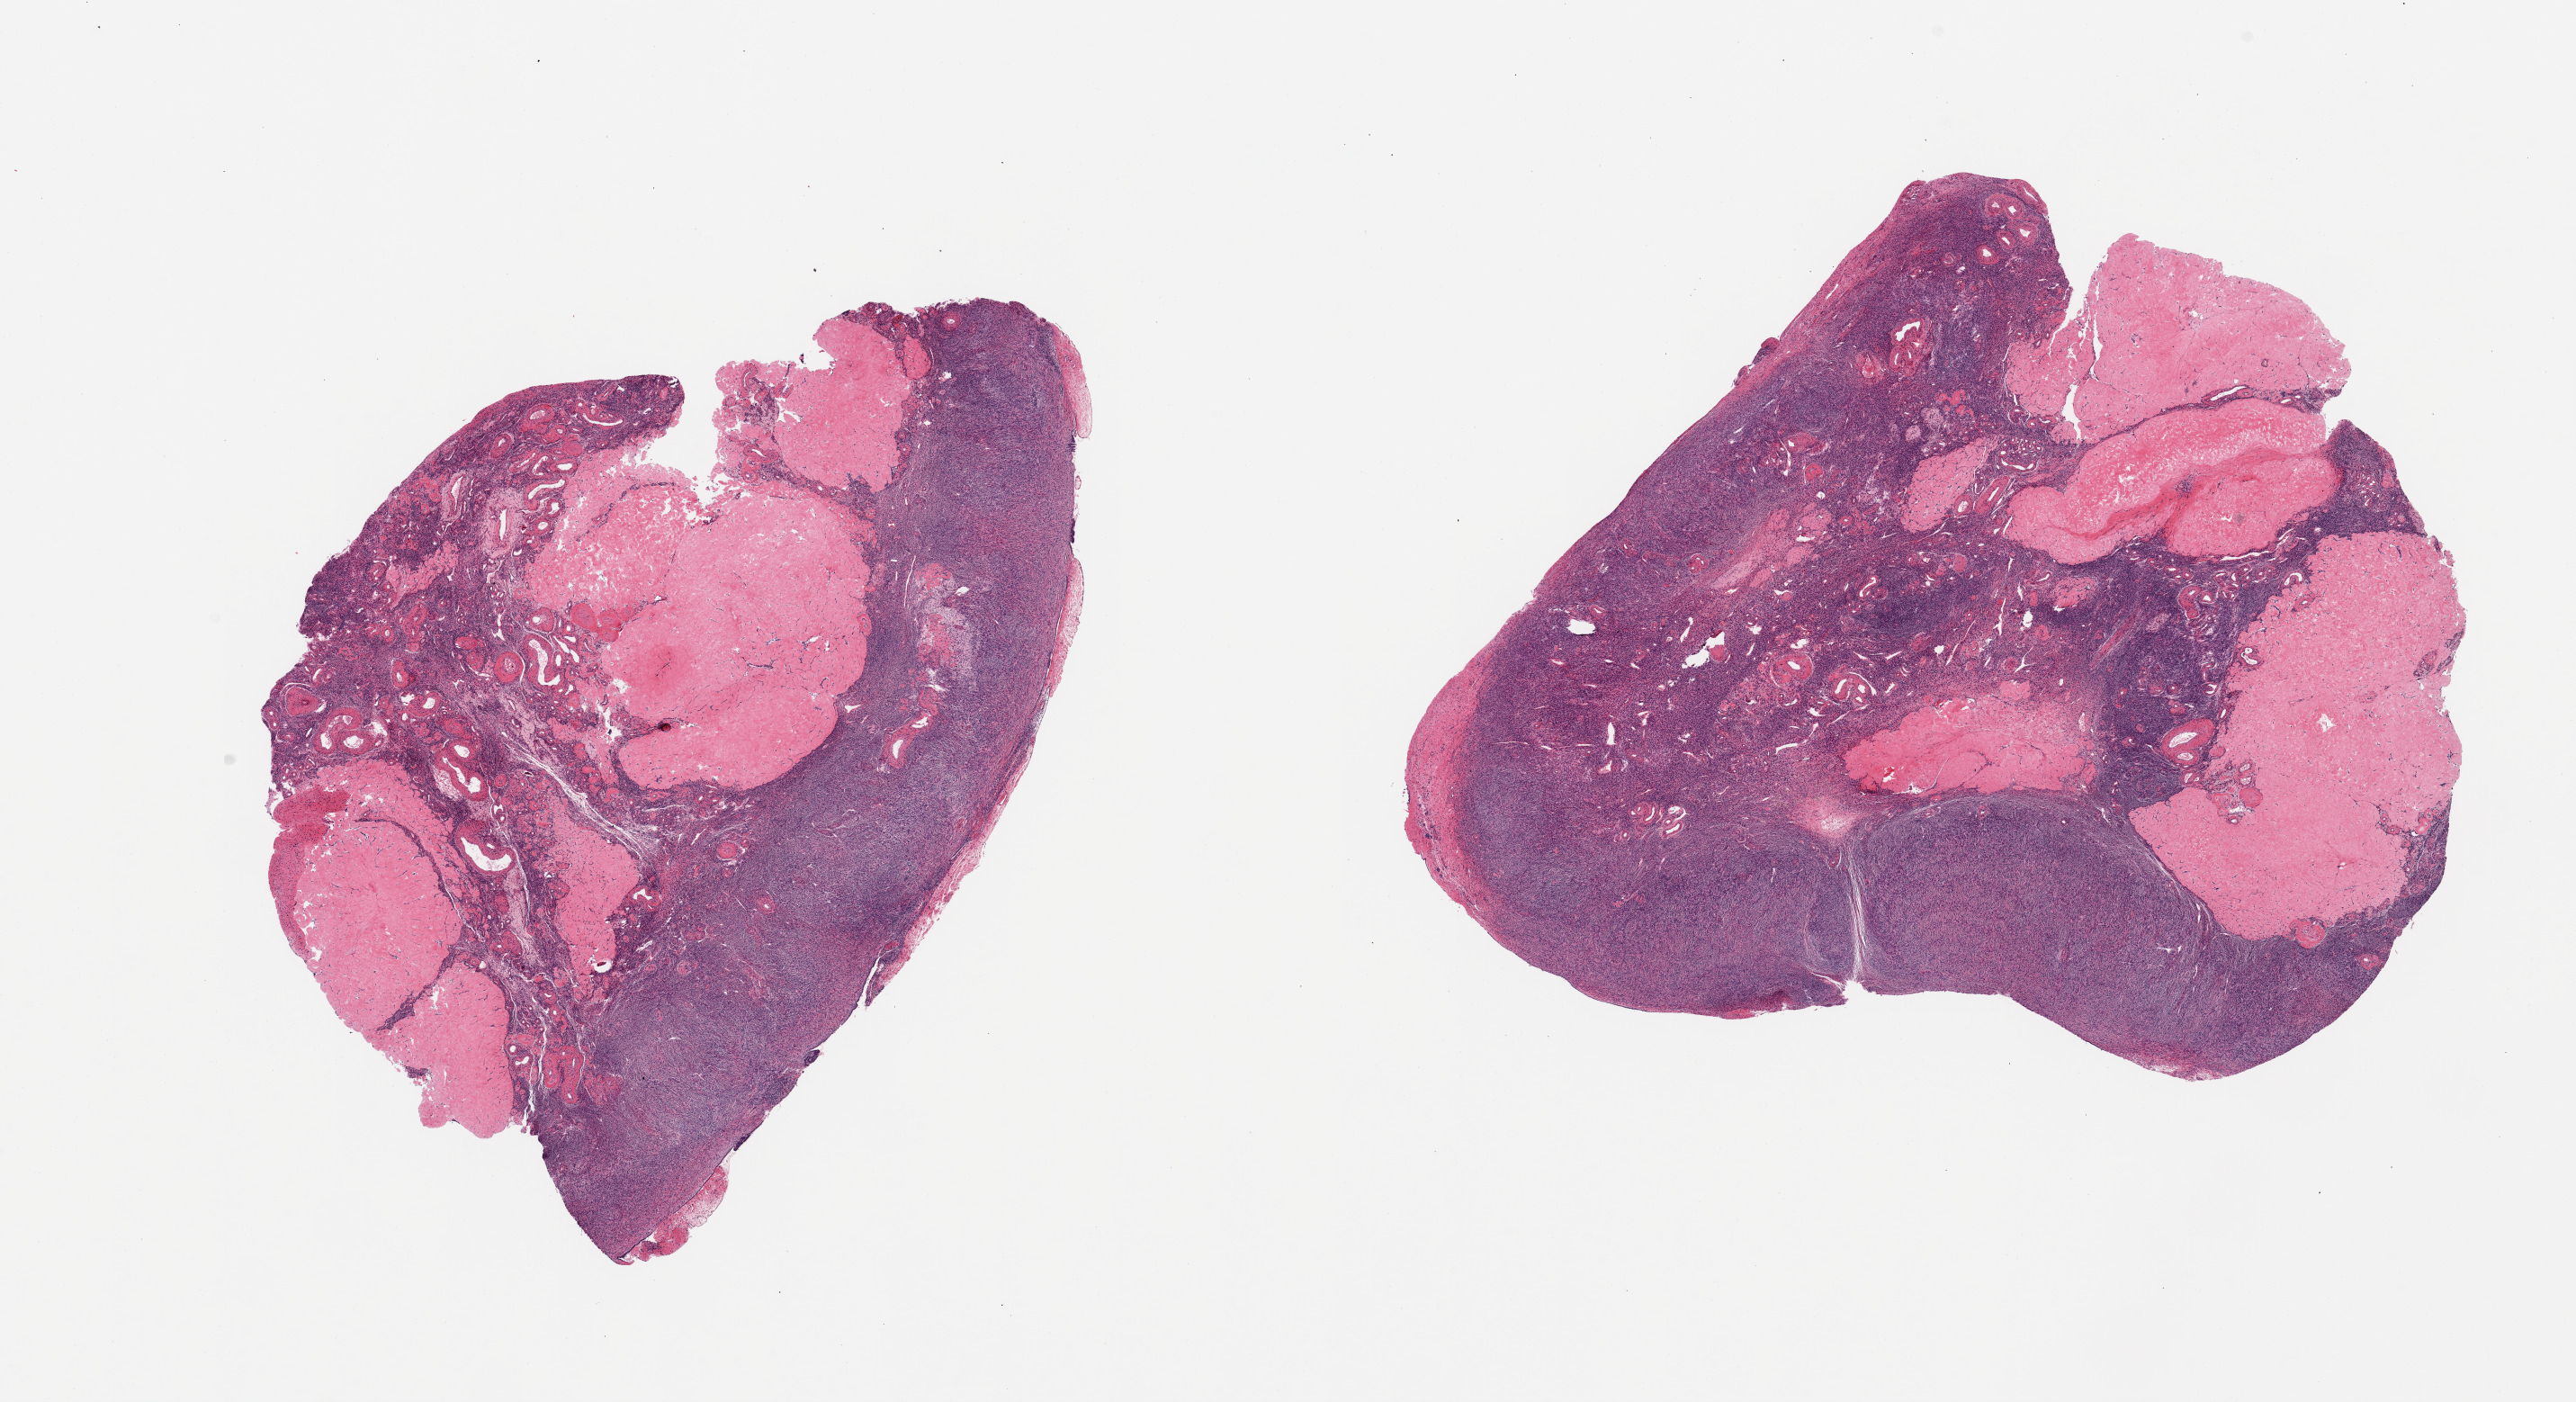
Digitized haematoxylin and eosin-stained section, brightfield — a low-resolution overview of the entire scanned area, about 22.6 x 12.3 mm (acquisition: 20x scan), PAXgene-fixed paraffin-embedded (PFPE) section, target tissue: ovary, donor tissue sample.
Reviewer comment on this tissue sample: 2 pieces; corpora albicantia occupy 50%.